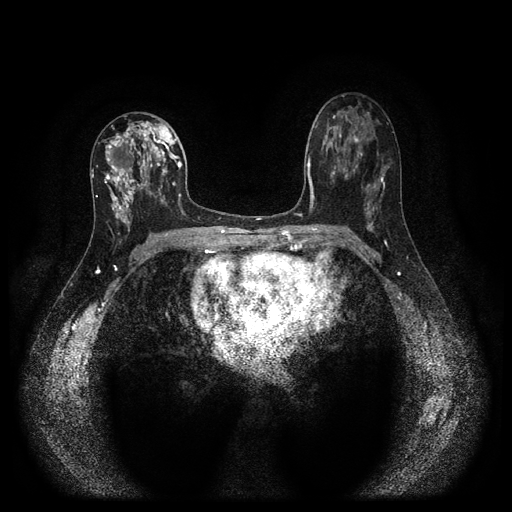
Breast MRI (dynamic contrast-enhanced, multi-phase), one axial slice; position 57 of 116 along the scan axis; dynamic contrast-enhanced series, time point 2 of 5 at this slice position (early post-contrast); 1.5 T; TE 2.7 ms, TR 5.4 ms; 512 × 512 image matrix. Patient: female, 47 years.
Annotated regions visible in this slice (semi-automatically segmented with operator editing):
- breast lesion (labelled 'tumour' in the annotation; benign lesions carry a separate 'benign' label): bounding box (x1, y1, x2, y2) in pixels: (98, 119, 172, 233)